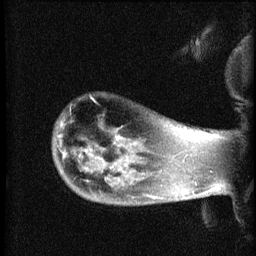
Breast MRI (dynamic contrast-enhanced), one sagittal slice. Slice 56 of 60 in the series (ordered by position). Dynamic contrast-enhanced series, image 2 of 3 at this slice position (ordered by acquisition). 1.5 T. TE 4.2 ms, TR 8.2 ms. 256 × 256 image matrix. Patient: female, 50 years.
Annotated regions visible in this slice (semi-automatic segmentation, software-assisted and operator-edited):
- analysis volume of interest (the breast-tissue region the enhancement analysis was run in; not a lesion): box from (x=53, y=116) to (x=169, y=205) px
- tumour enhancement mask (voxels above the 70 % enhancement threshold inside the analysis volume of interest): (x=152, y=197)–(x=154, y=199)